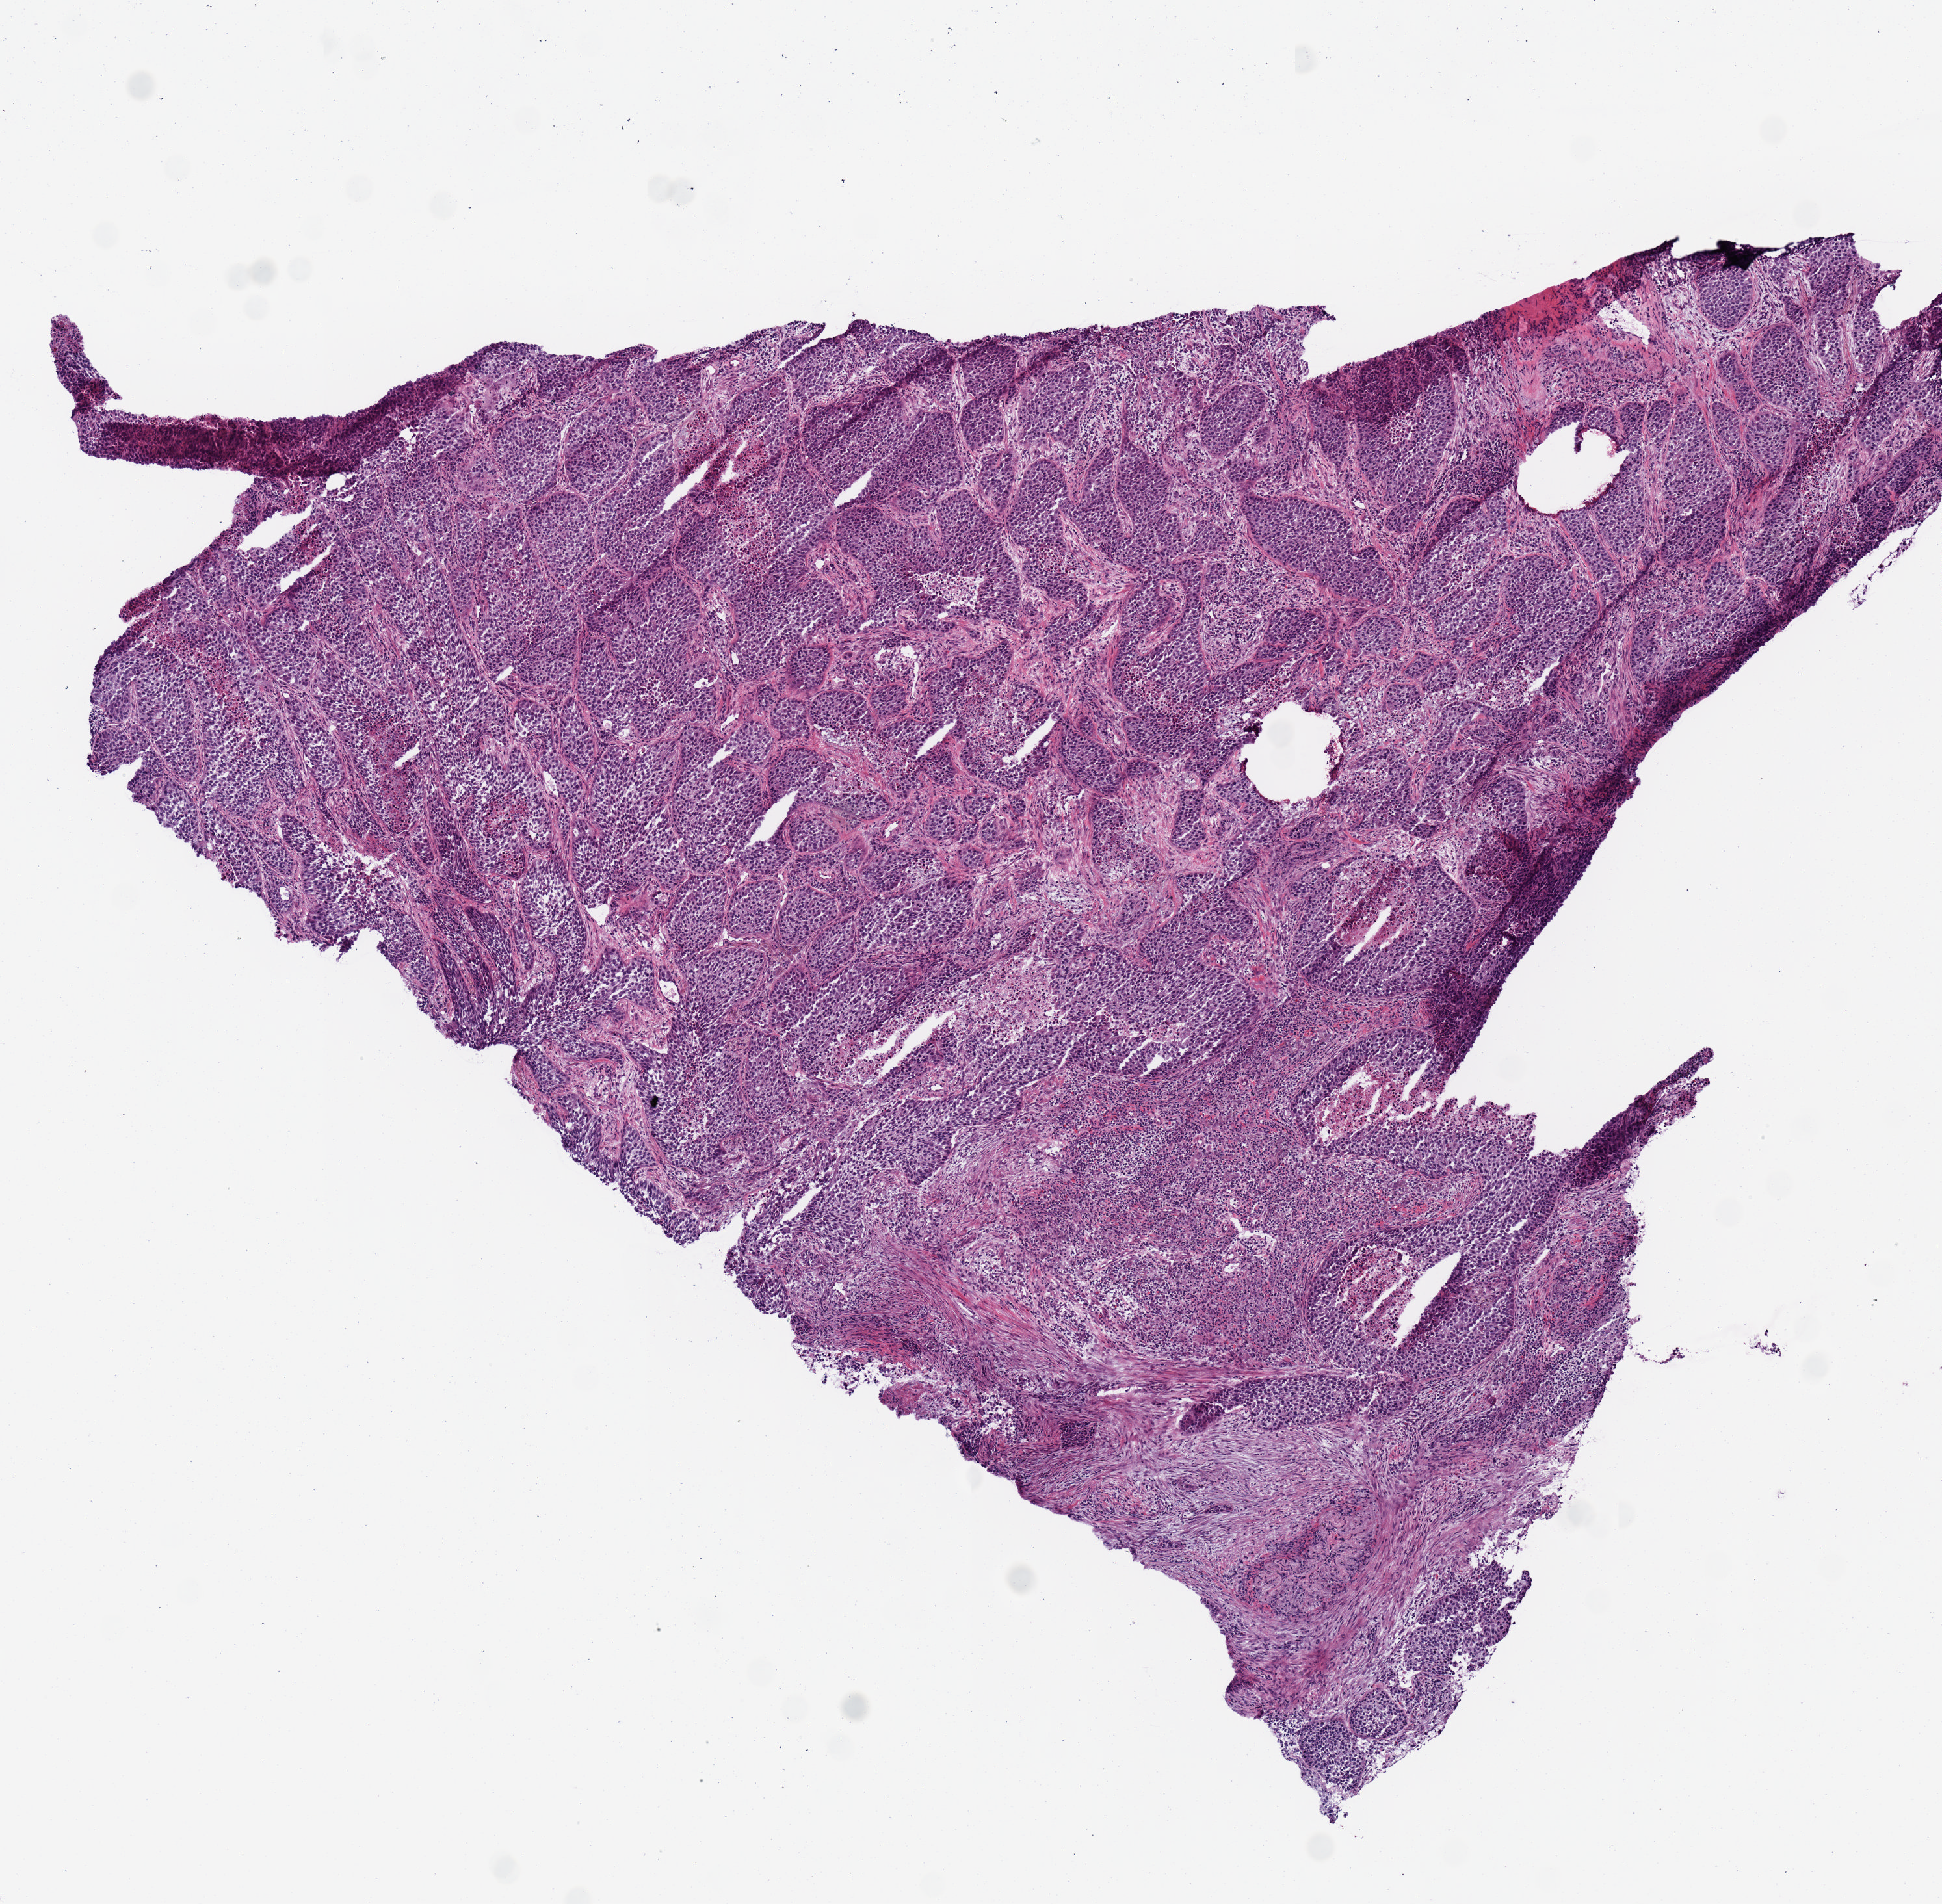
Whole-slide histology image, H&E — a low-resolution overview of the entire scanned area, about 5.9 x 5.8 mm; frozen section; lung, primary tumour sample. Patient: male, age at initial diagnosis 66 years. Slide review estimates, as recorded: tumour cells 0%, tumour nuclei 80%.
Diagnosis: Squamous cell carcinoma, NOS (upper lobe, lung).